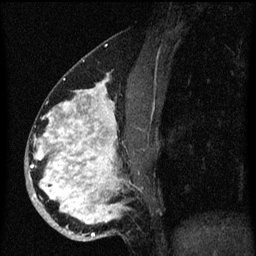
Breast MRI (dynamic contrast-enhanced), one sagittal slice. Position 29 of 60 along the scan axis. Dynamic contrast-enhanced series, image 2 of 3 at this slice position (ordered by acquisition). 1.5 T. TE 4.2 ms, TR 8.4 ms. 256 × 256 image matrix, field of view 180 × 180 mm. Patient: female, 34 years. From the clinical record (not read from this slice): setting: breast cancer imaged before/during neoadjuvant chemotherapy; receptor status: HR-positive, HER2-negative.
Annotated regions visible in this slice (semi-automatically segmented with operator editing):
- analysis volume of interest (the breast-tissue region the enhancement analysis was run in; not a lesion): bounding box (x1, y1, x2, y2) in pixels: (26, 58, 145, 241)
- tumour enhancement mask (voxels above the 70 % enhancement threshold inside the analysis volume of interest): (30, 78, 125, 239)